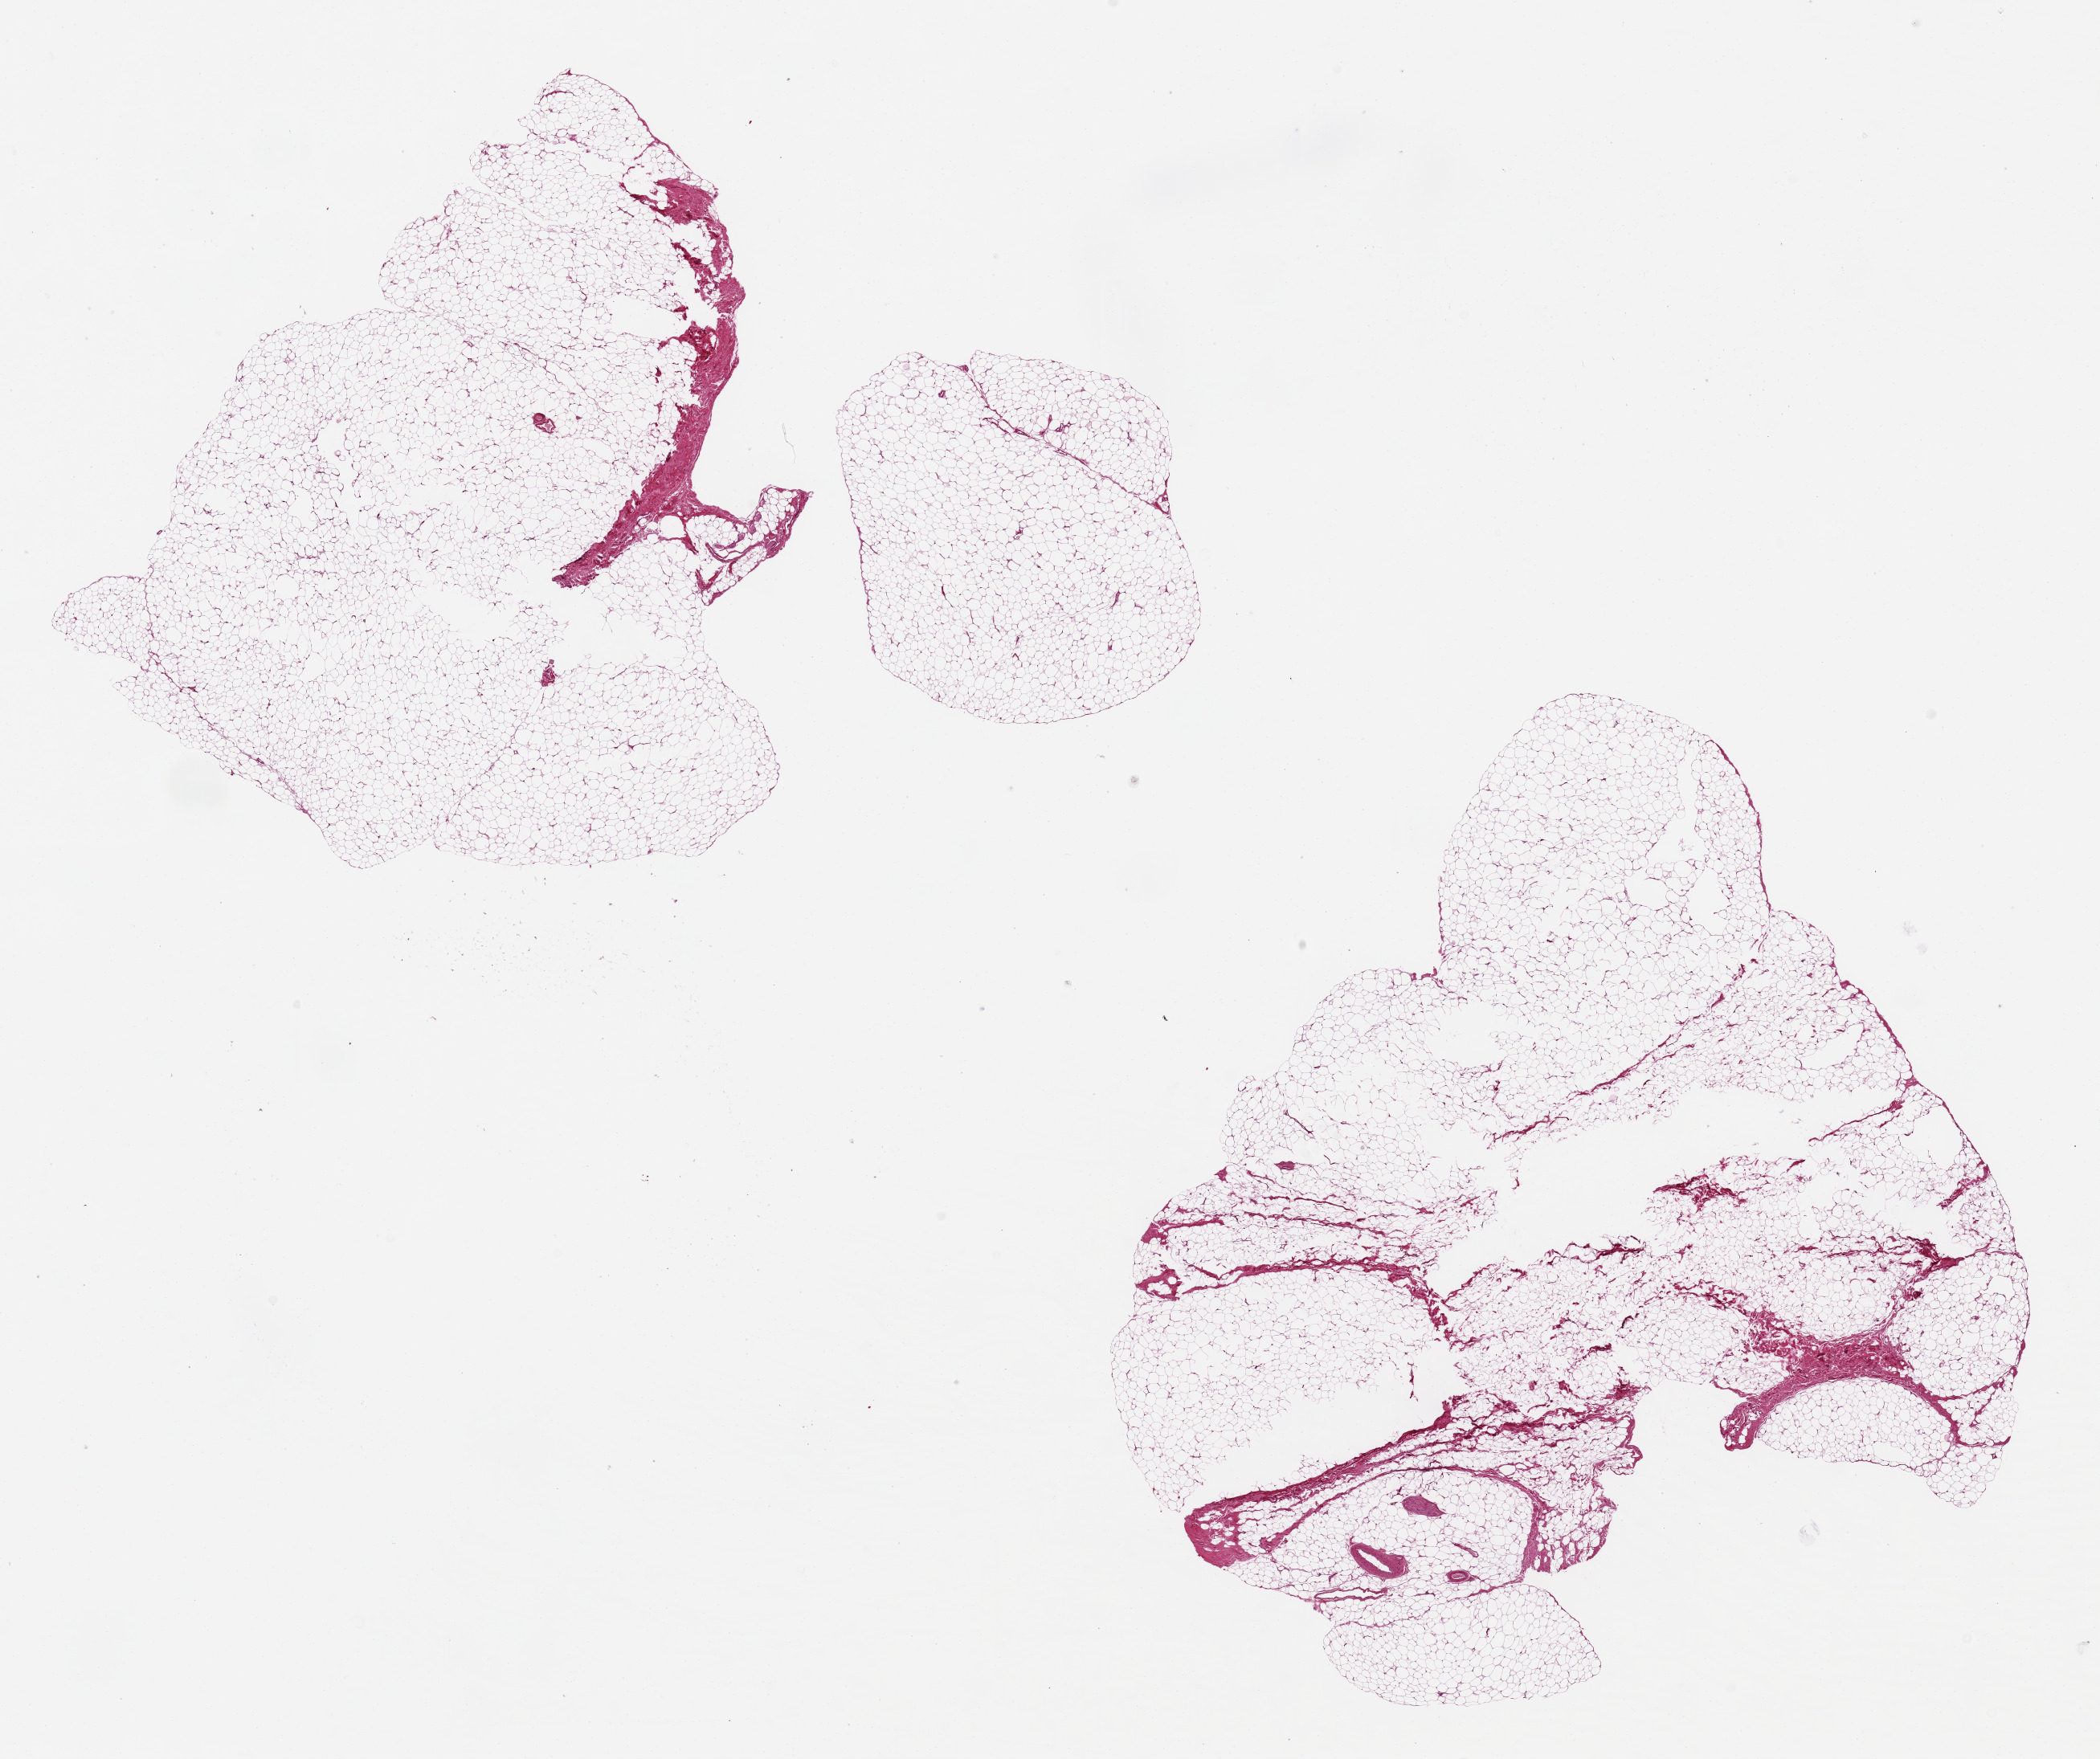
Whole-slide image, hematoxylin and eosin (H&E) stain, brightfield, whole scanned area (about 20.7 x 17.3 mm) shown as a low-resolution overview; PAXgene-fixed, paraffin-embedded tissue; section of breast (target tissue); tissue donor sample. Donor: male.
• review note (as recorded): 2 aliquots, ~8x8mm. No ductal elements noted